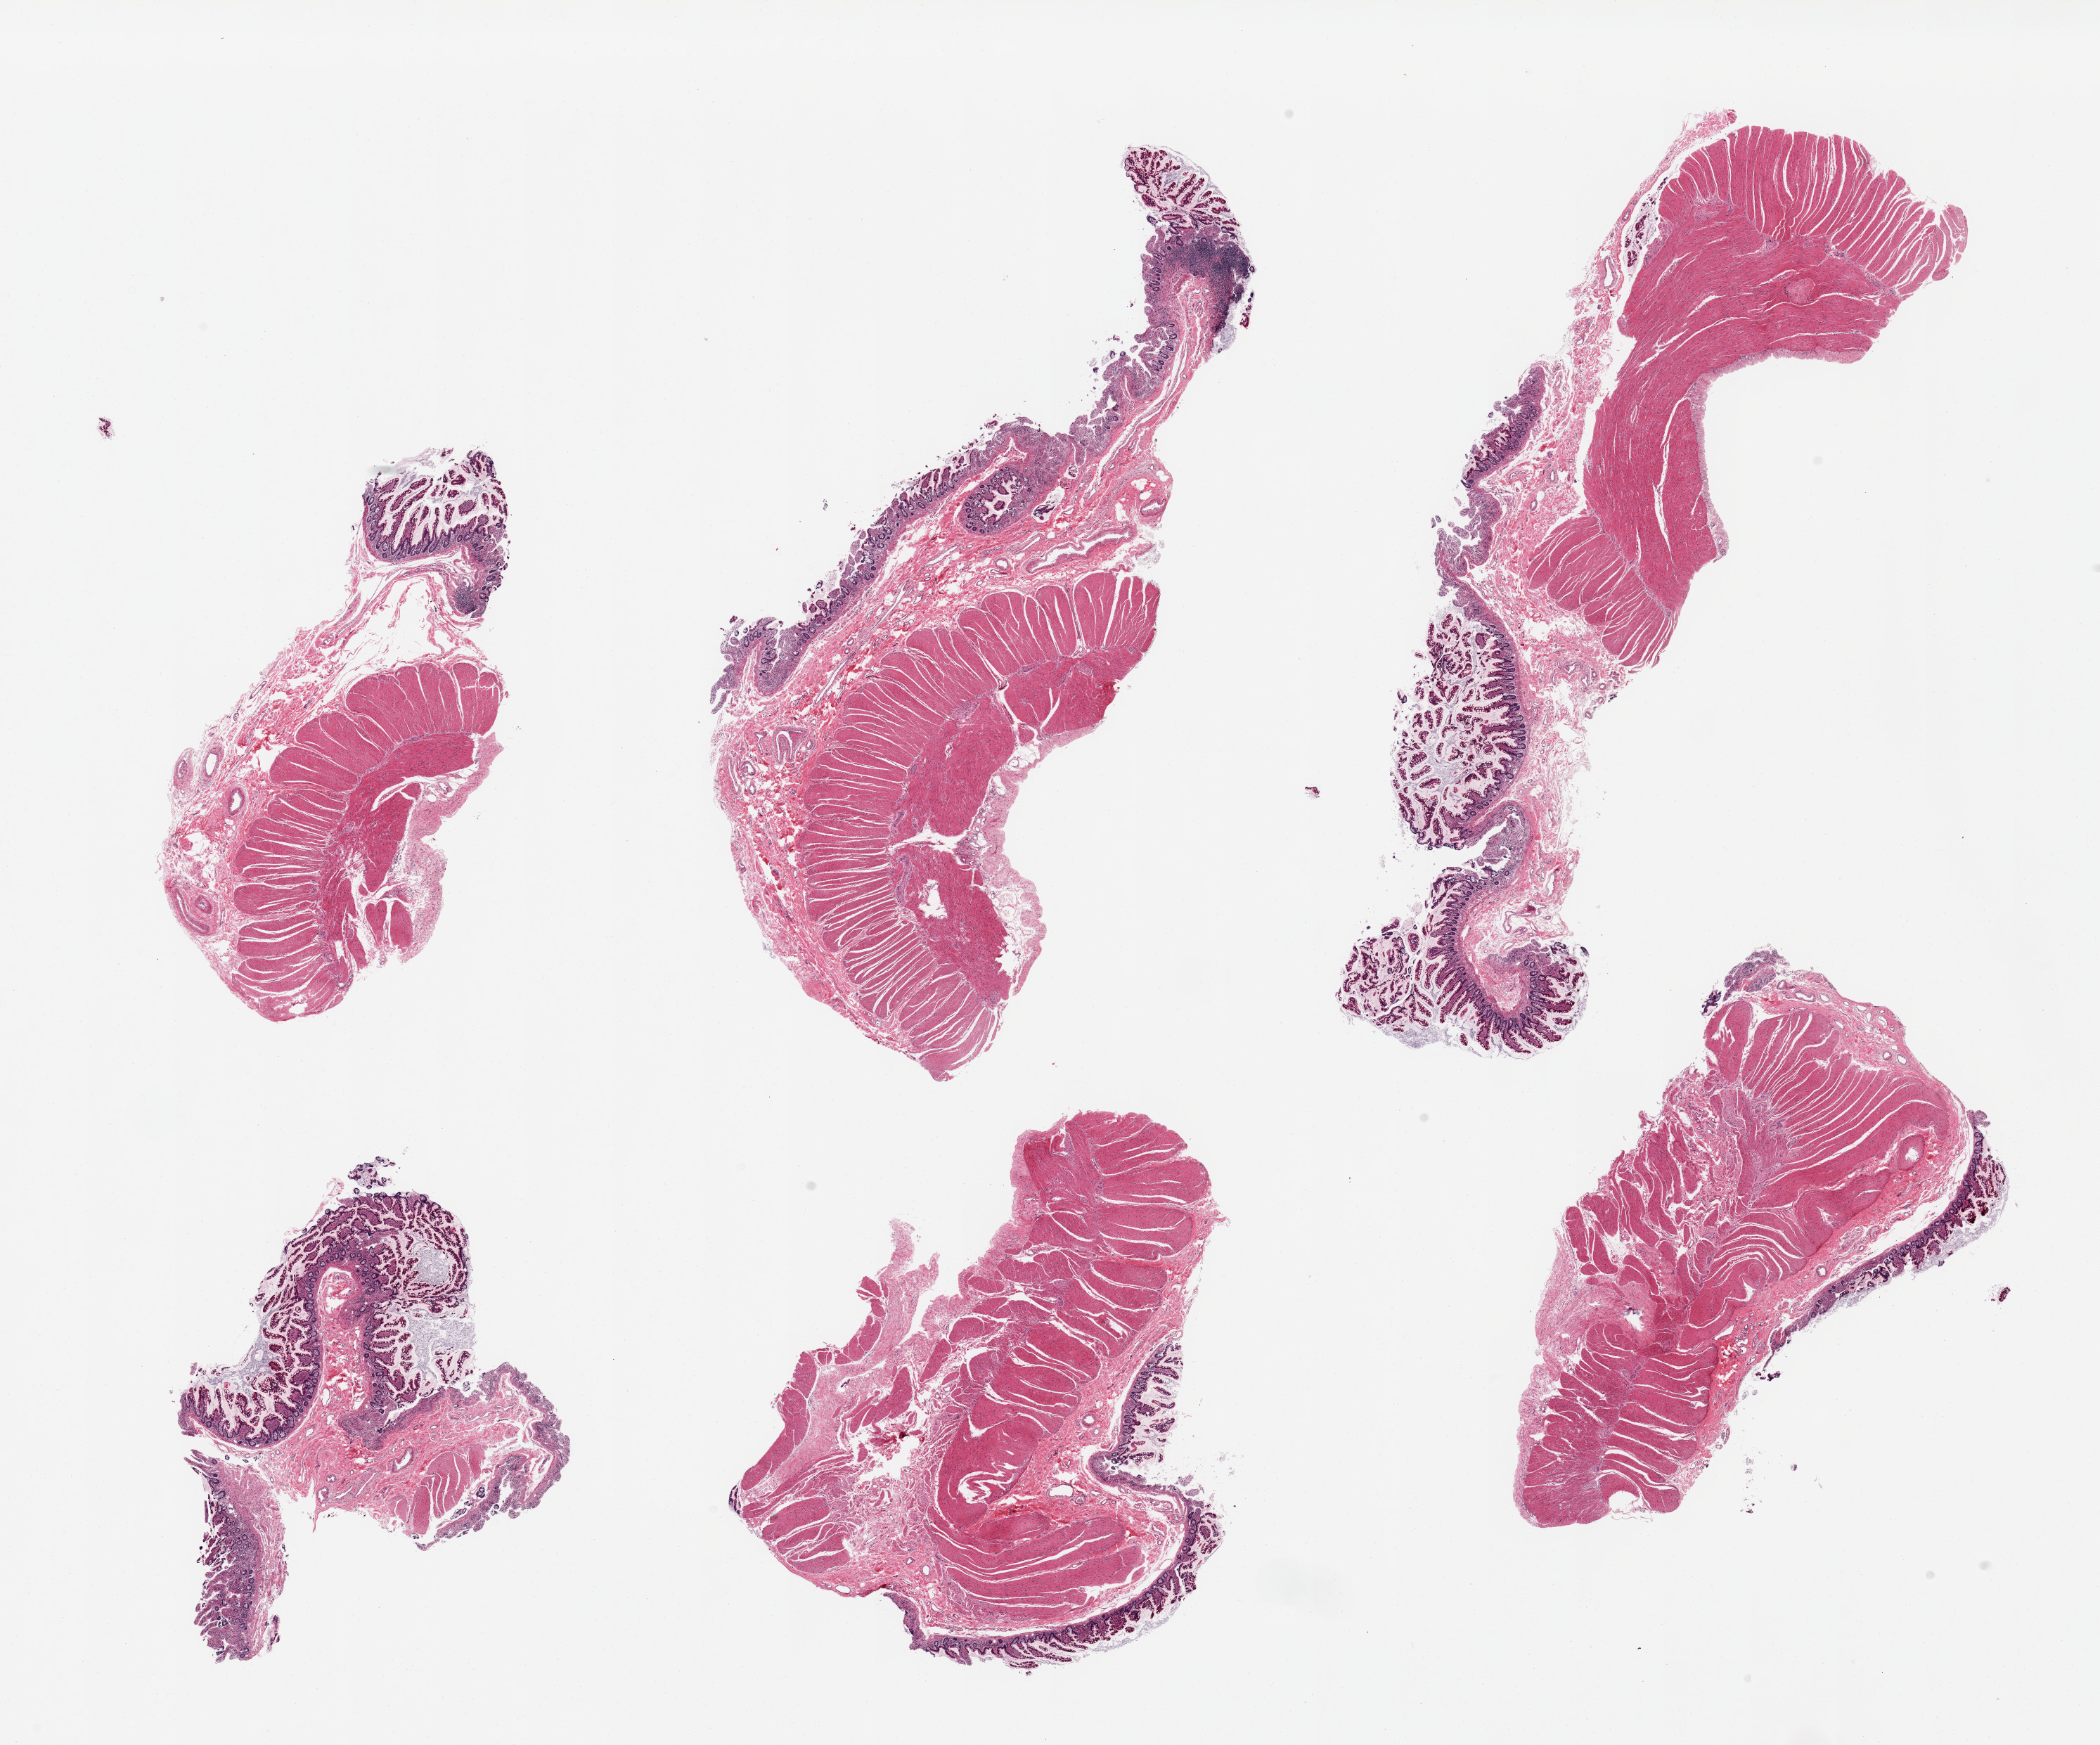
Whole-slide image, haematoxylin and eosin stain, brightfield, low-resolution overview of the scanned area, about 23.6 x 19.6 mm (slide scanned at 20x), PAXgene-fixed, paraffin-embedded tissue, section of ileum (target tissue), donor tissue sample. Female donor.
* pathologist's review note for this sample: 6 pieces; only 1 has lymphoid tissue and it is a tiny, 1mm, focus; also is full thickness bowel wall (not target)